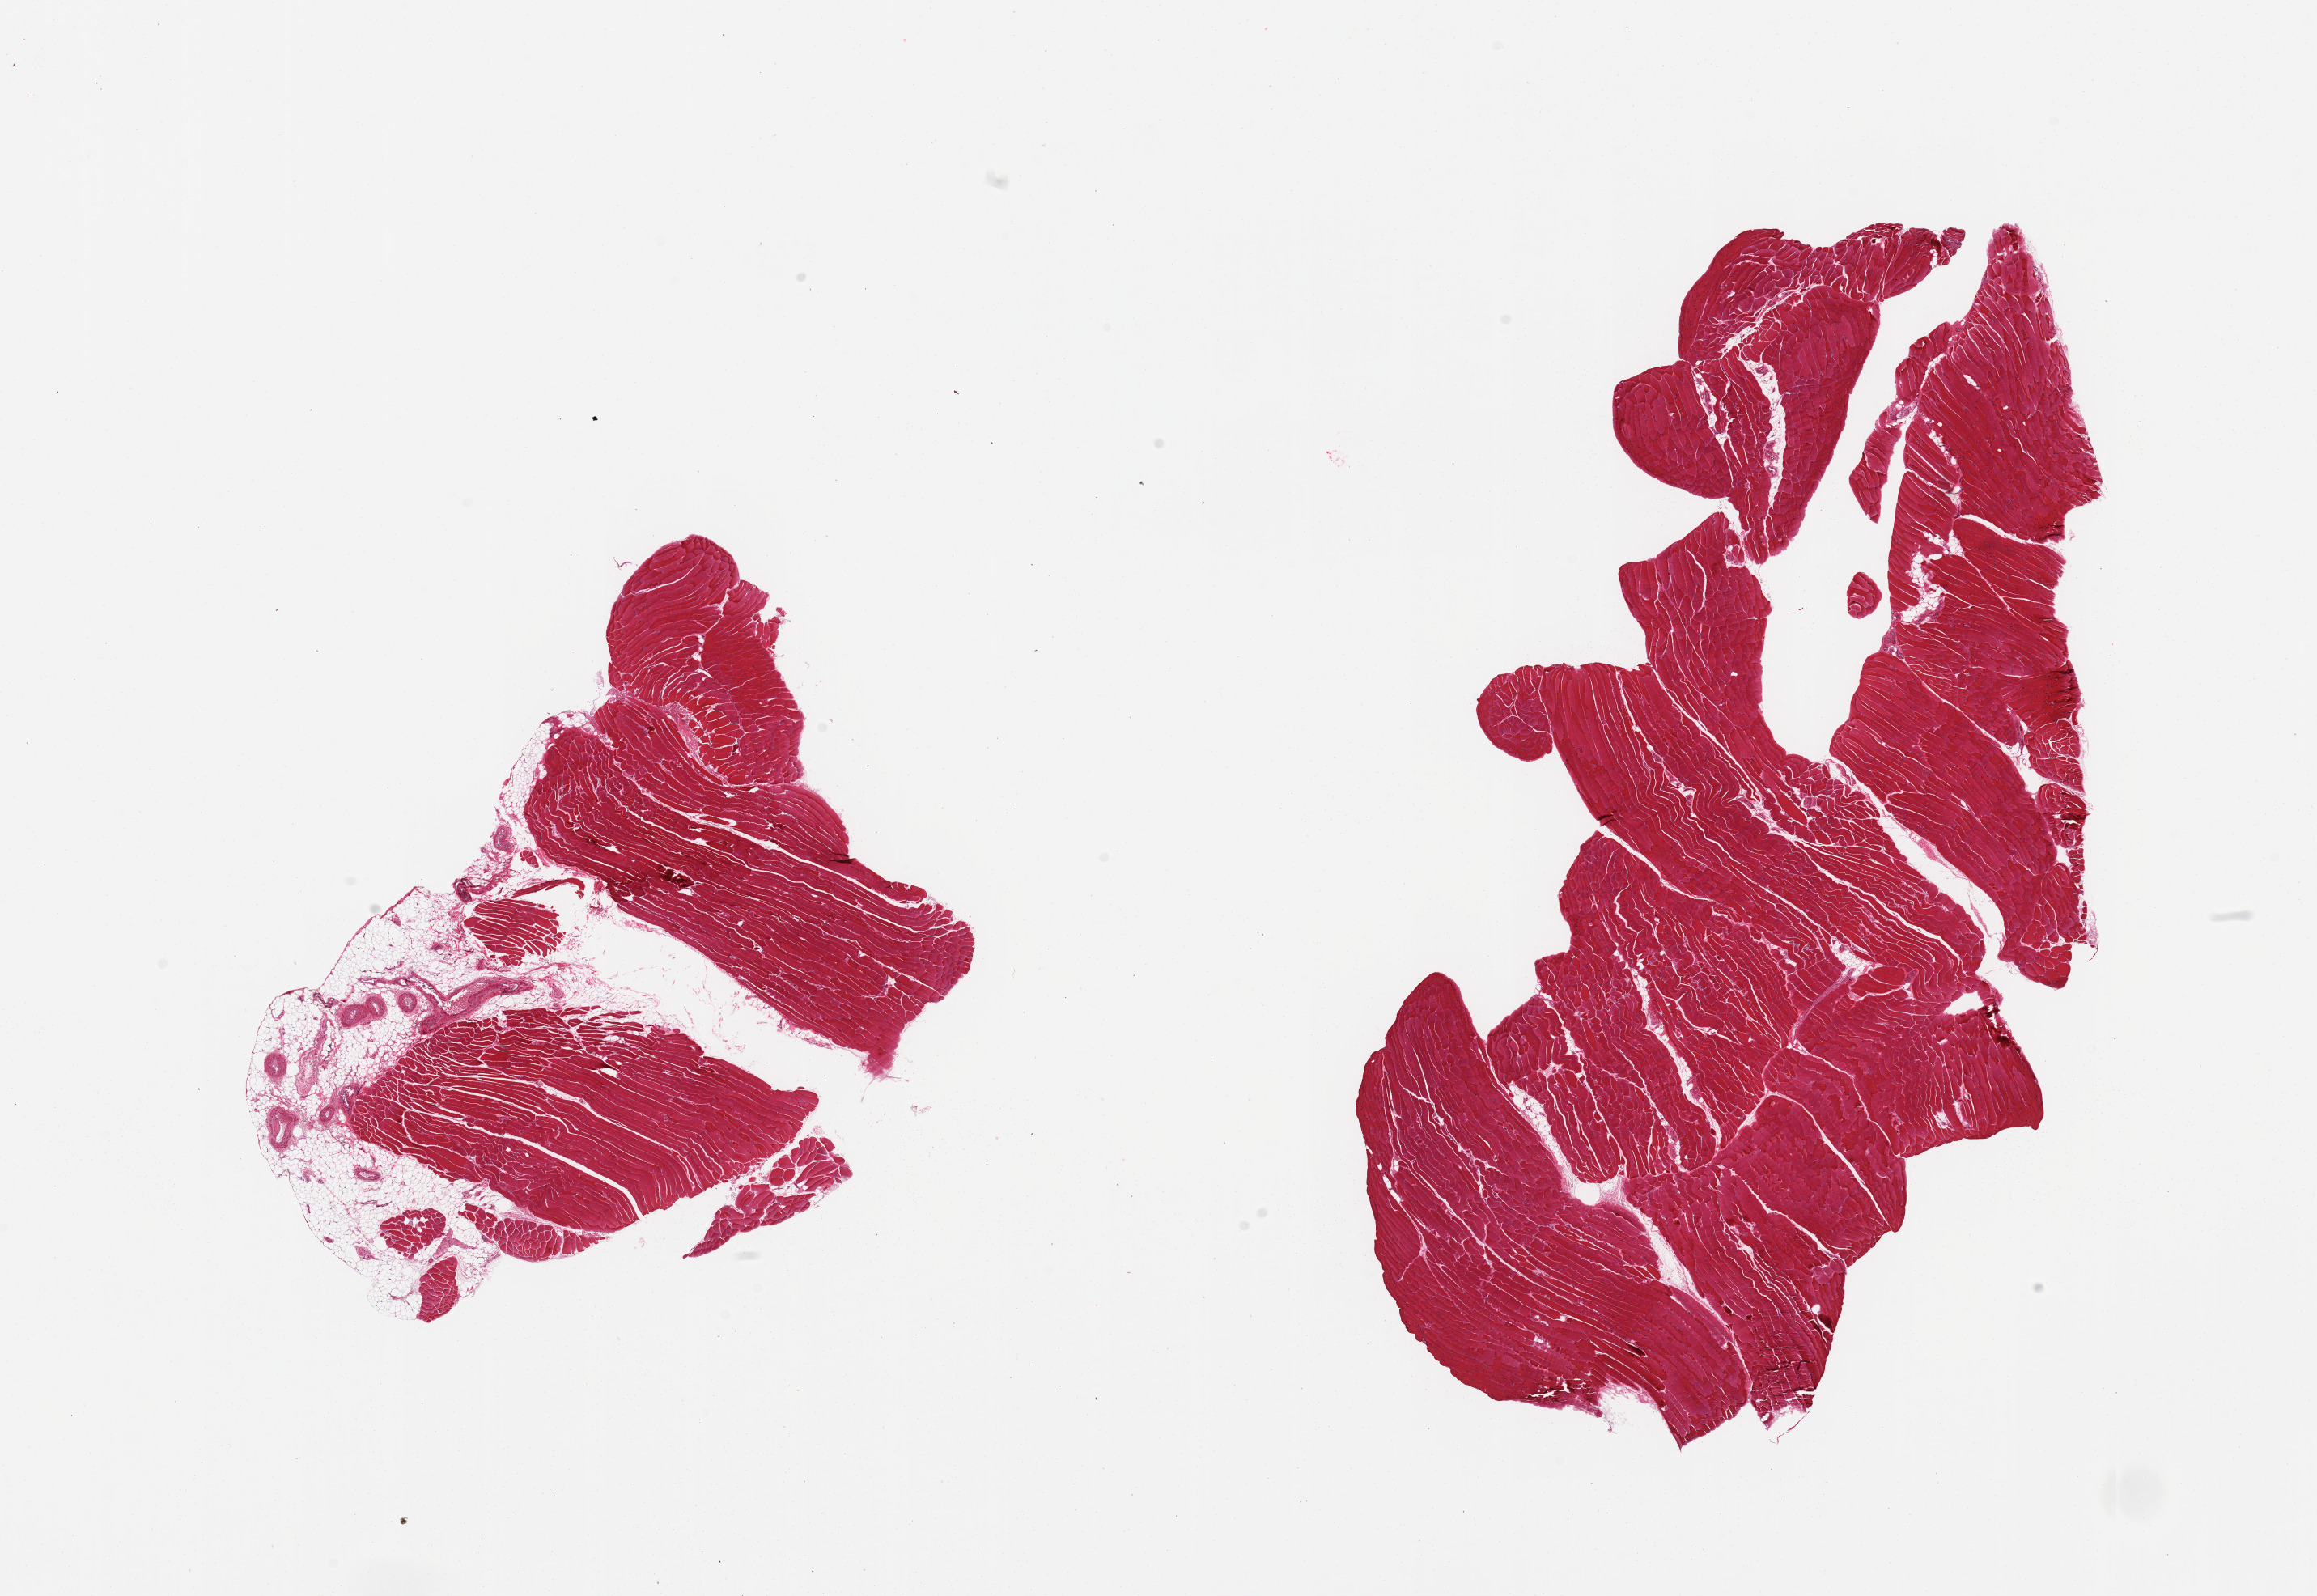
Haematoxylin and eosin whole-slide image, brightfield — a low-resolution overview of the entire scanned area, about 22.6 x 15.6 mm (acquisition: 20x scan), PAXgene-fixed paraffin-embedded (PFPE) section, sampled site (target tissue): skeletal muscle, donor tissue sample. Female donor.
• reviewer comment on this tissue sample: 2 pieces; 1 piece includes ~30% attachment of fat/vessels/nerve